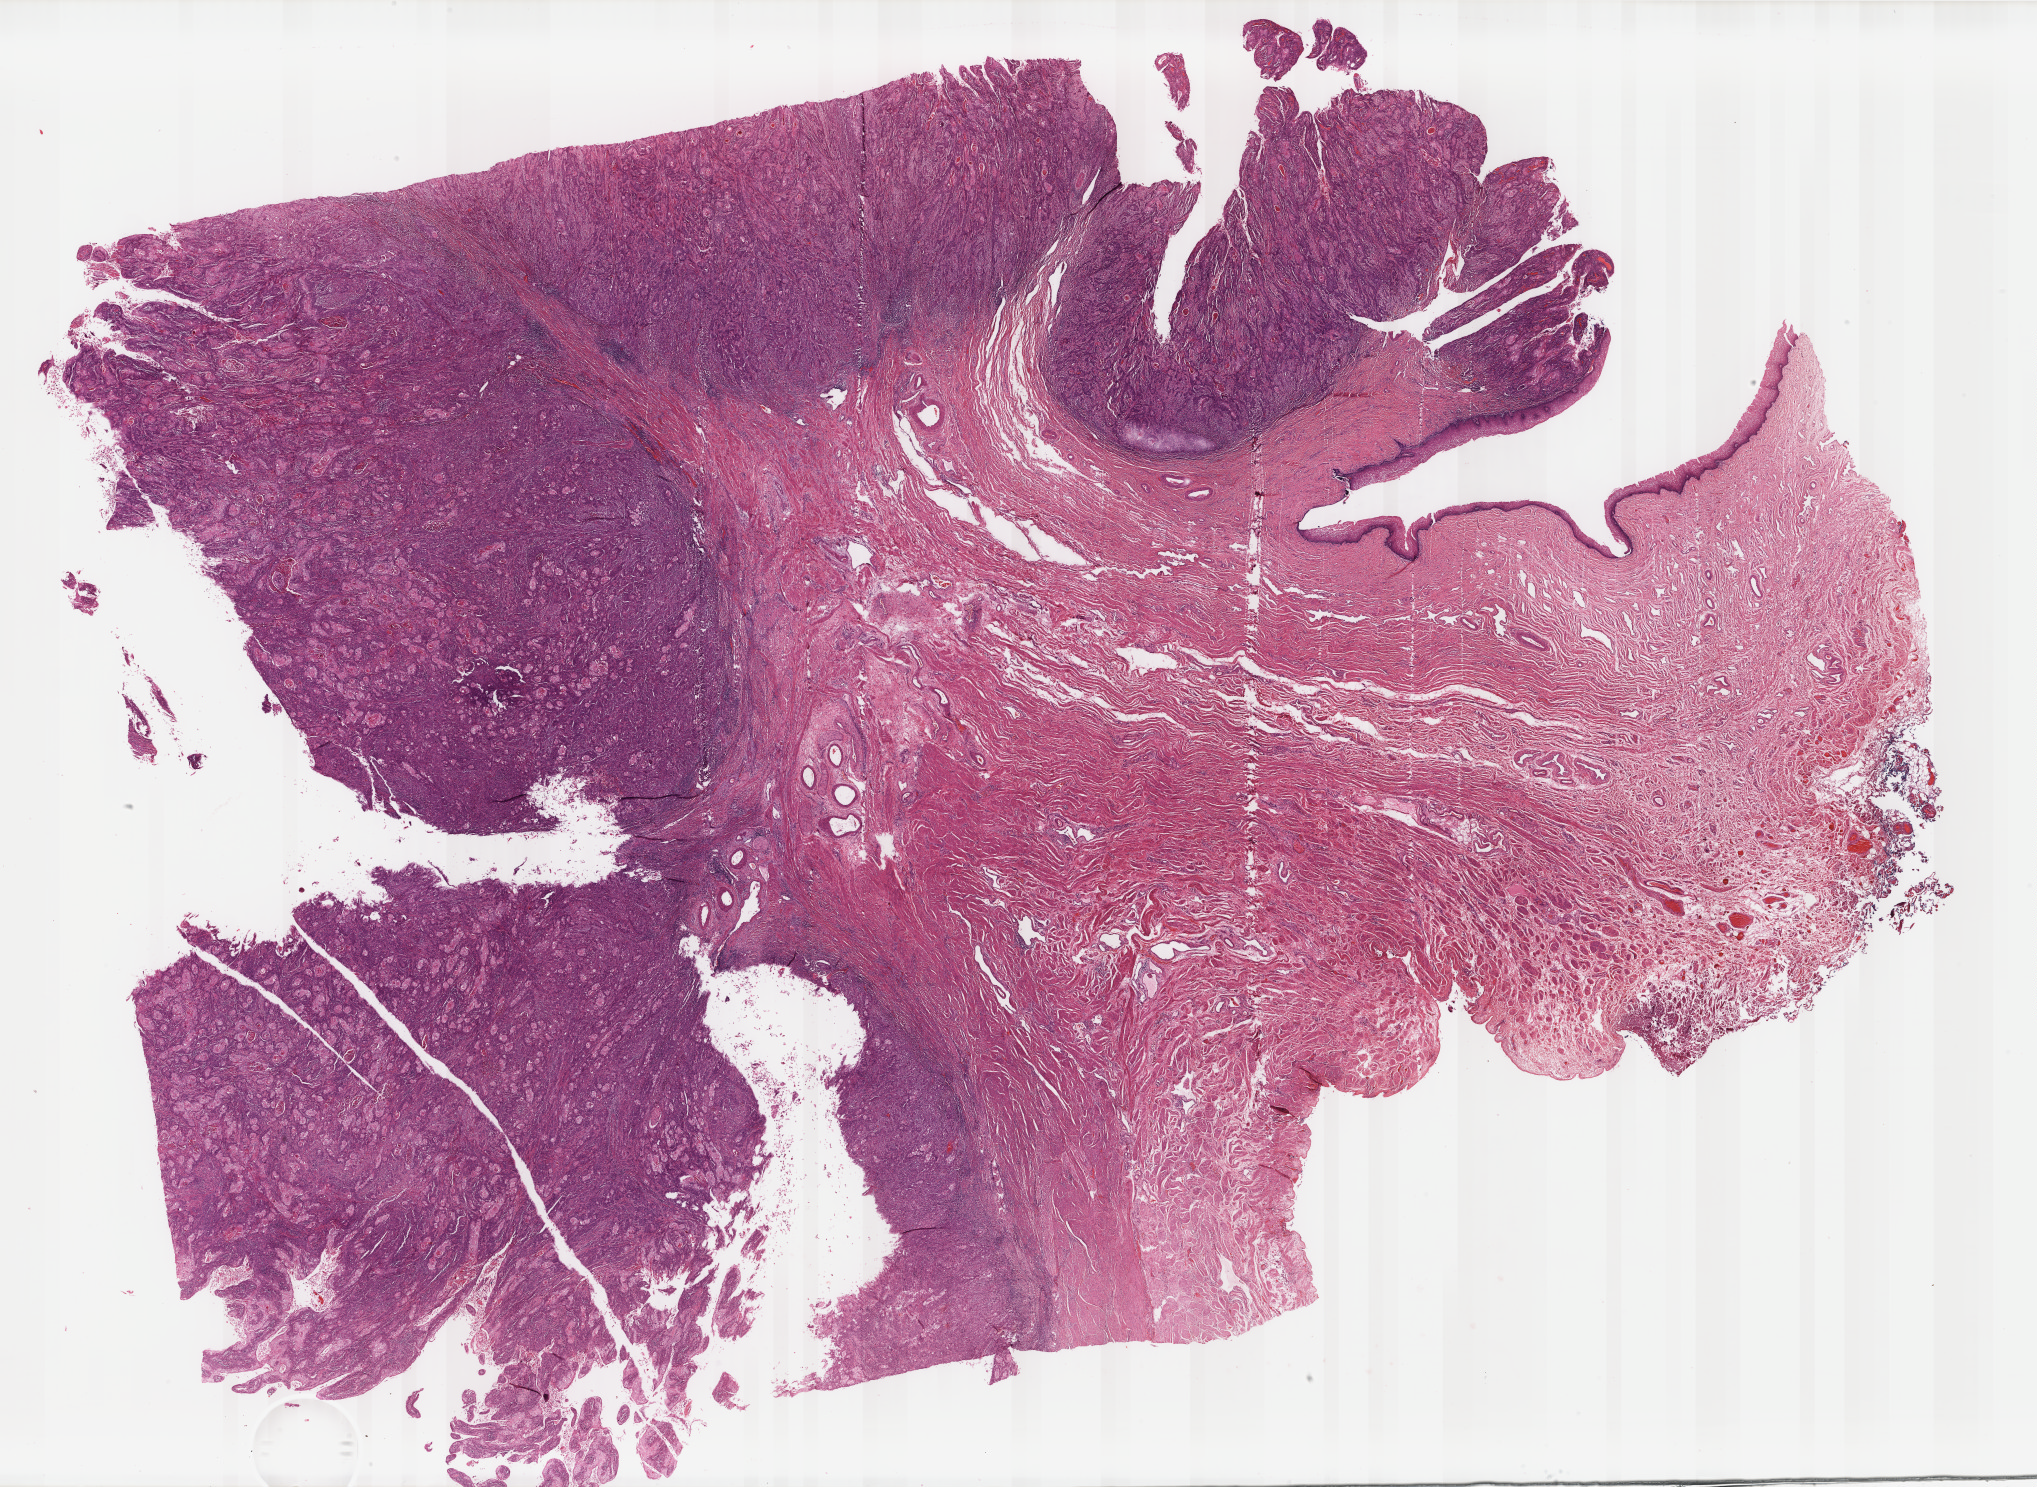
Whole-slide histology image, Hematoxylin and eosin (H&E) stained, whole scanned area (about 32.3 x 23.6 mm) shown as a low-resolution overview; formalin-fixed paraffin-embedded (FFPE) diagnostic section; sample: primary tumour, cervix. Female, age 47 years at initial diagnosis. Histologic grade: G2 (moderately differentiated).
• pathologic diagnosis: Squamous cell carcinoma, NOS
• lymph nodes positive (case pathology): 0 of 19 examined